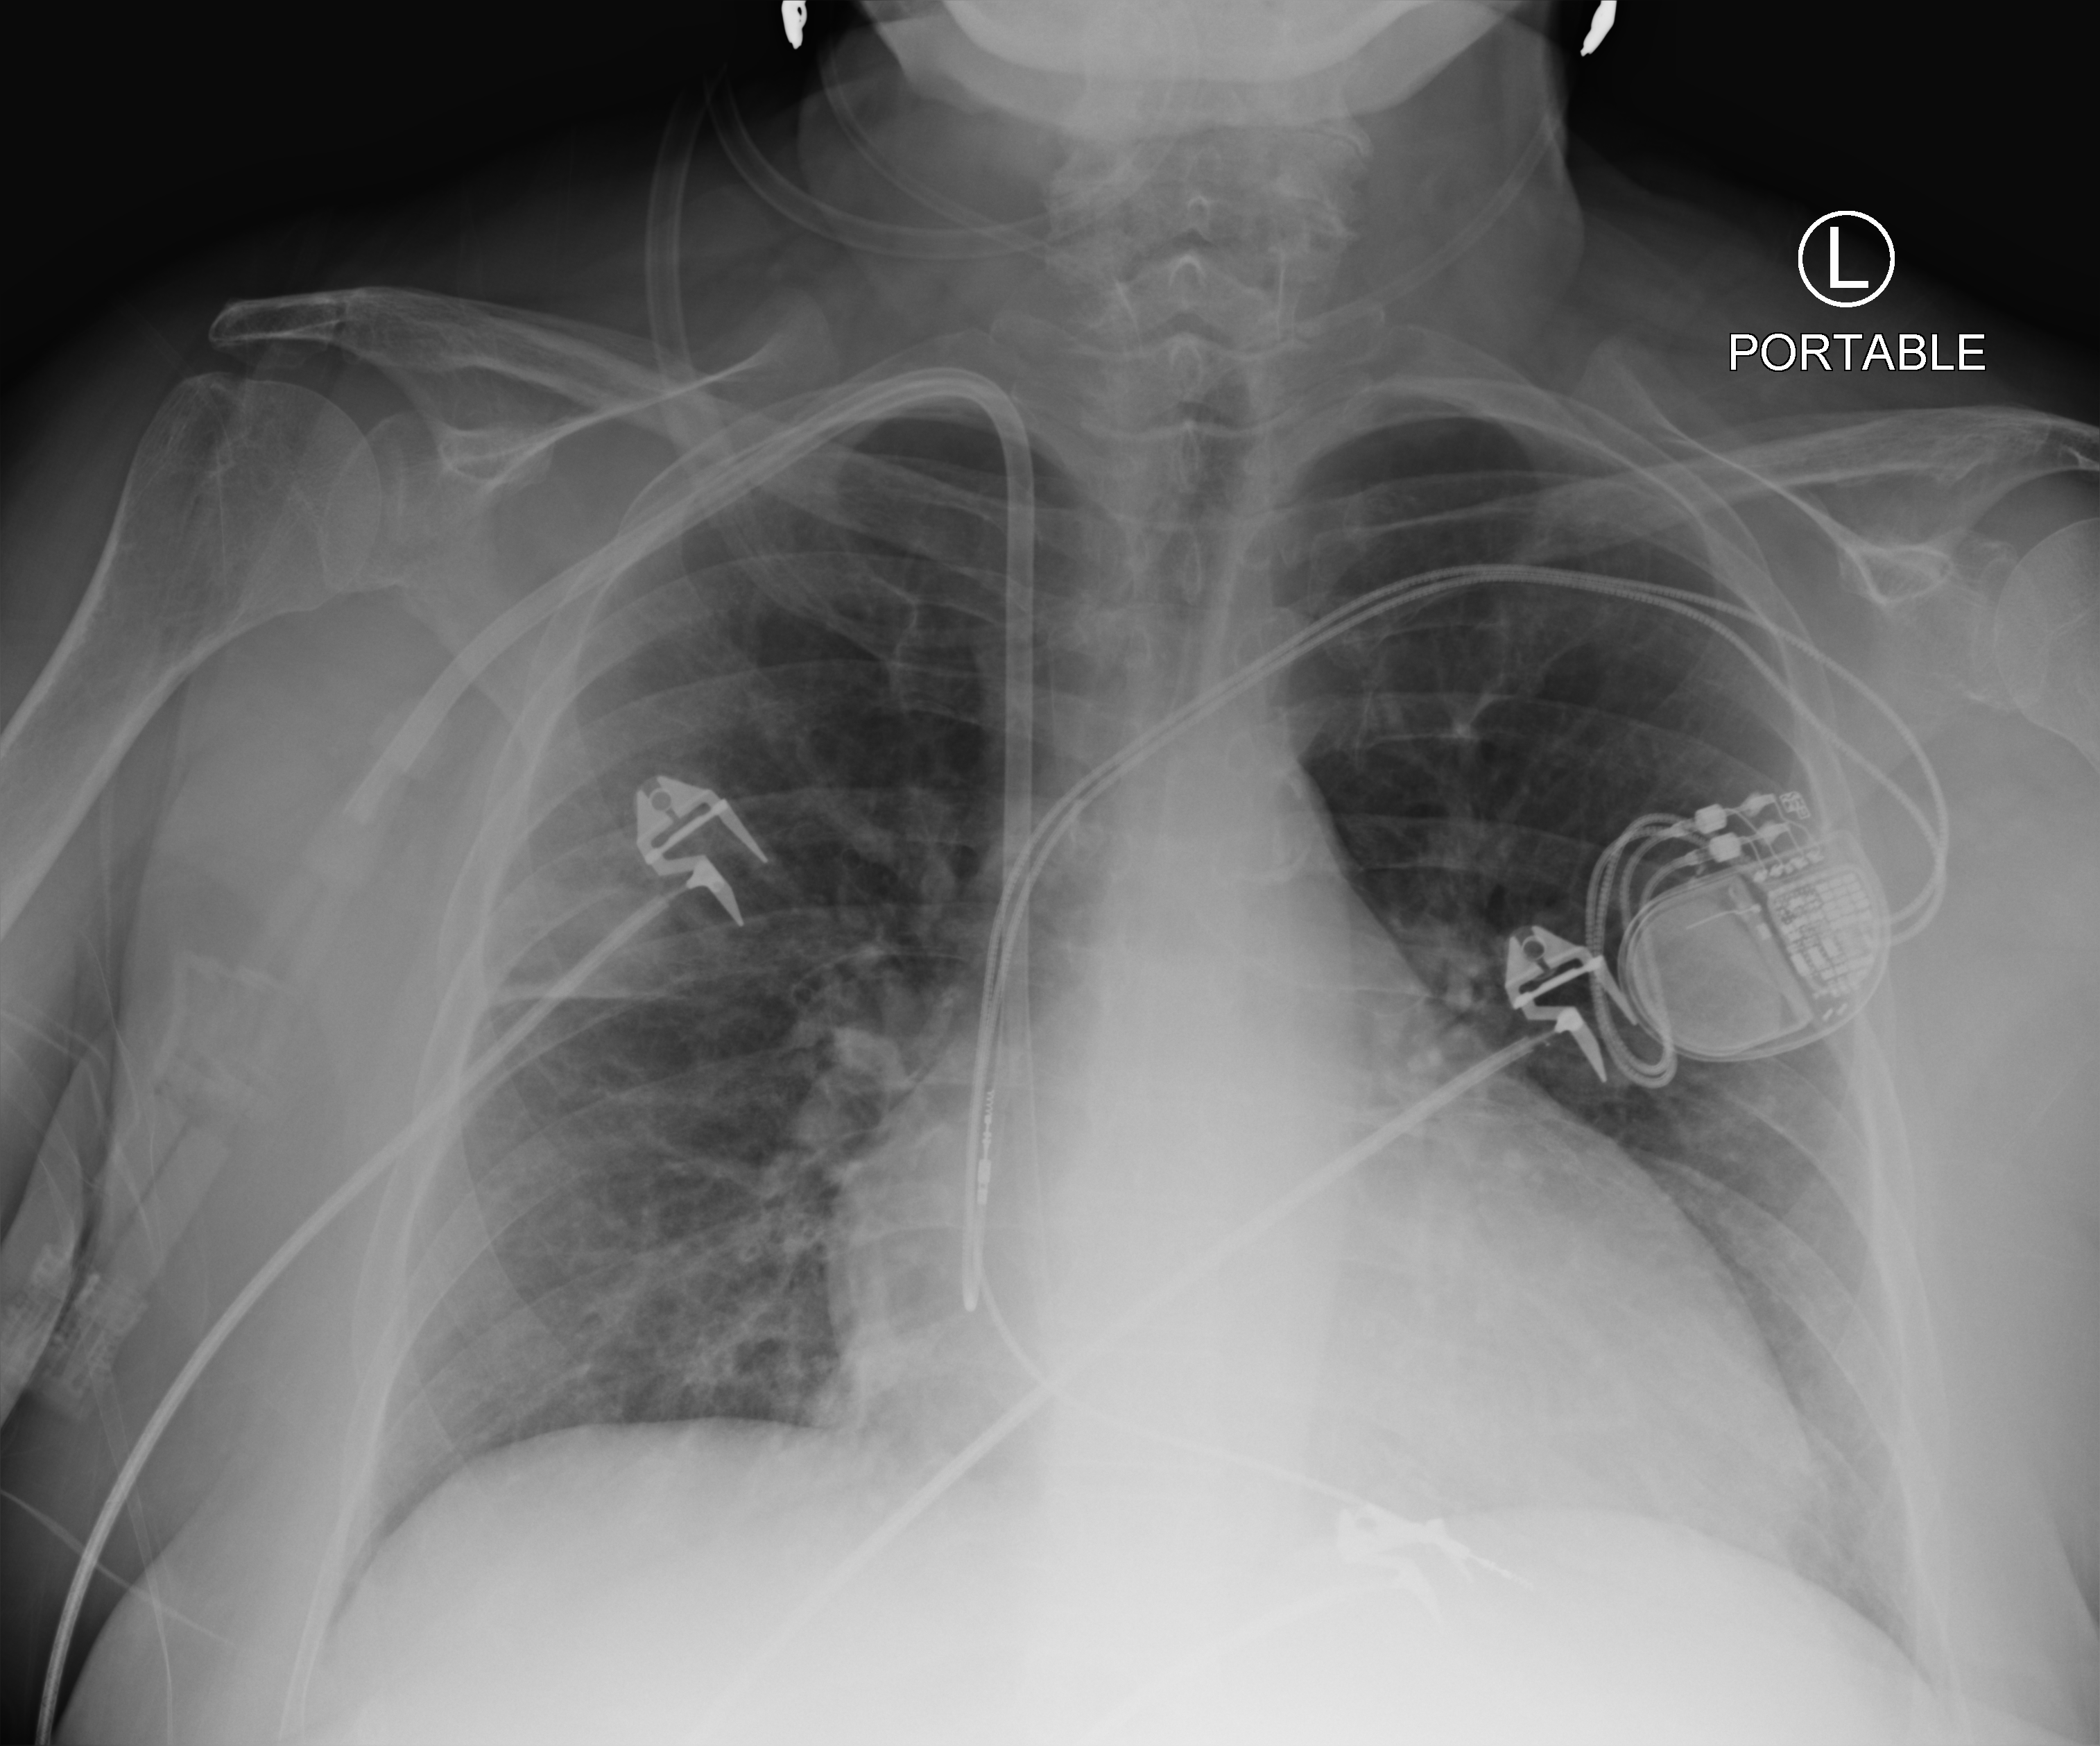
Portable chest radiograph; anteroposterior (AP) projection. Patient hospitalised with COVID-19; female, aged 60–74 years.
Admission-level facts for this patient (not findings on this image; timing relative to this image not recorded): mechanically ventilated during this hospital stay: no; admitted to intensive care during this hospital stay: no.